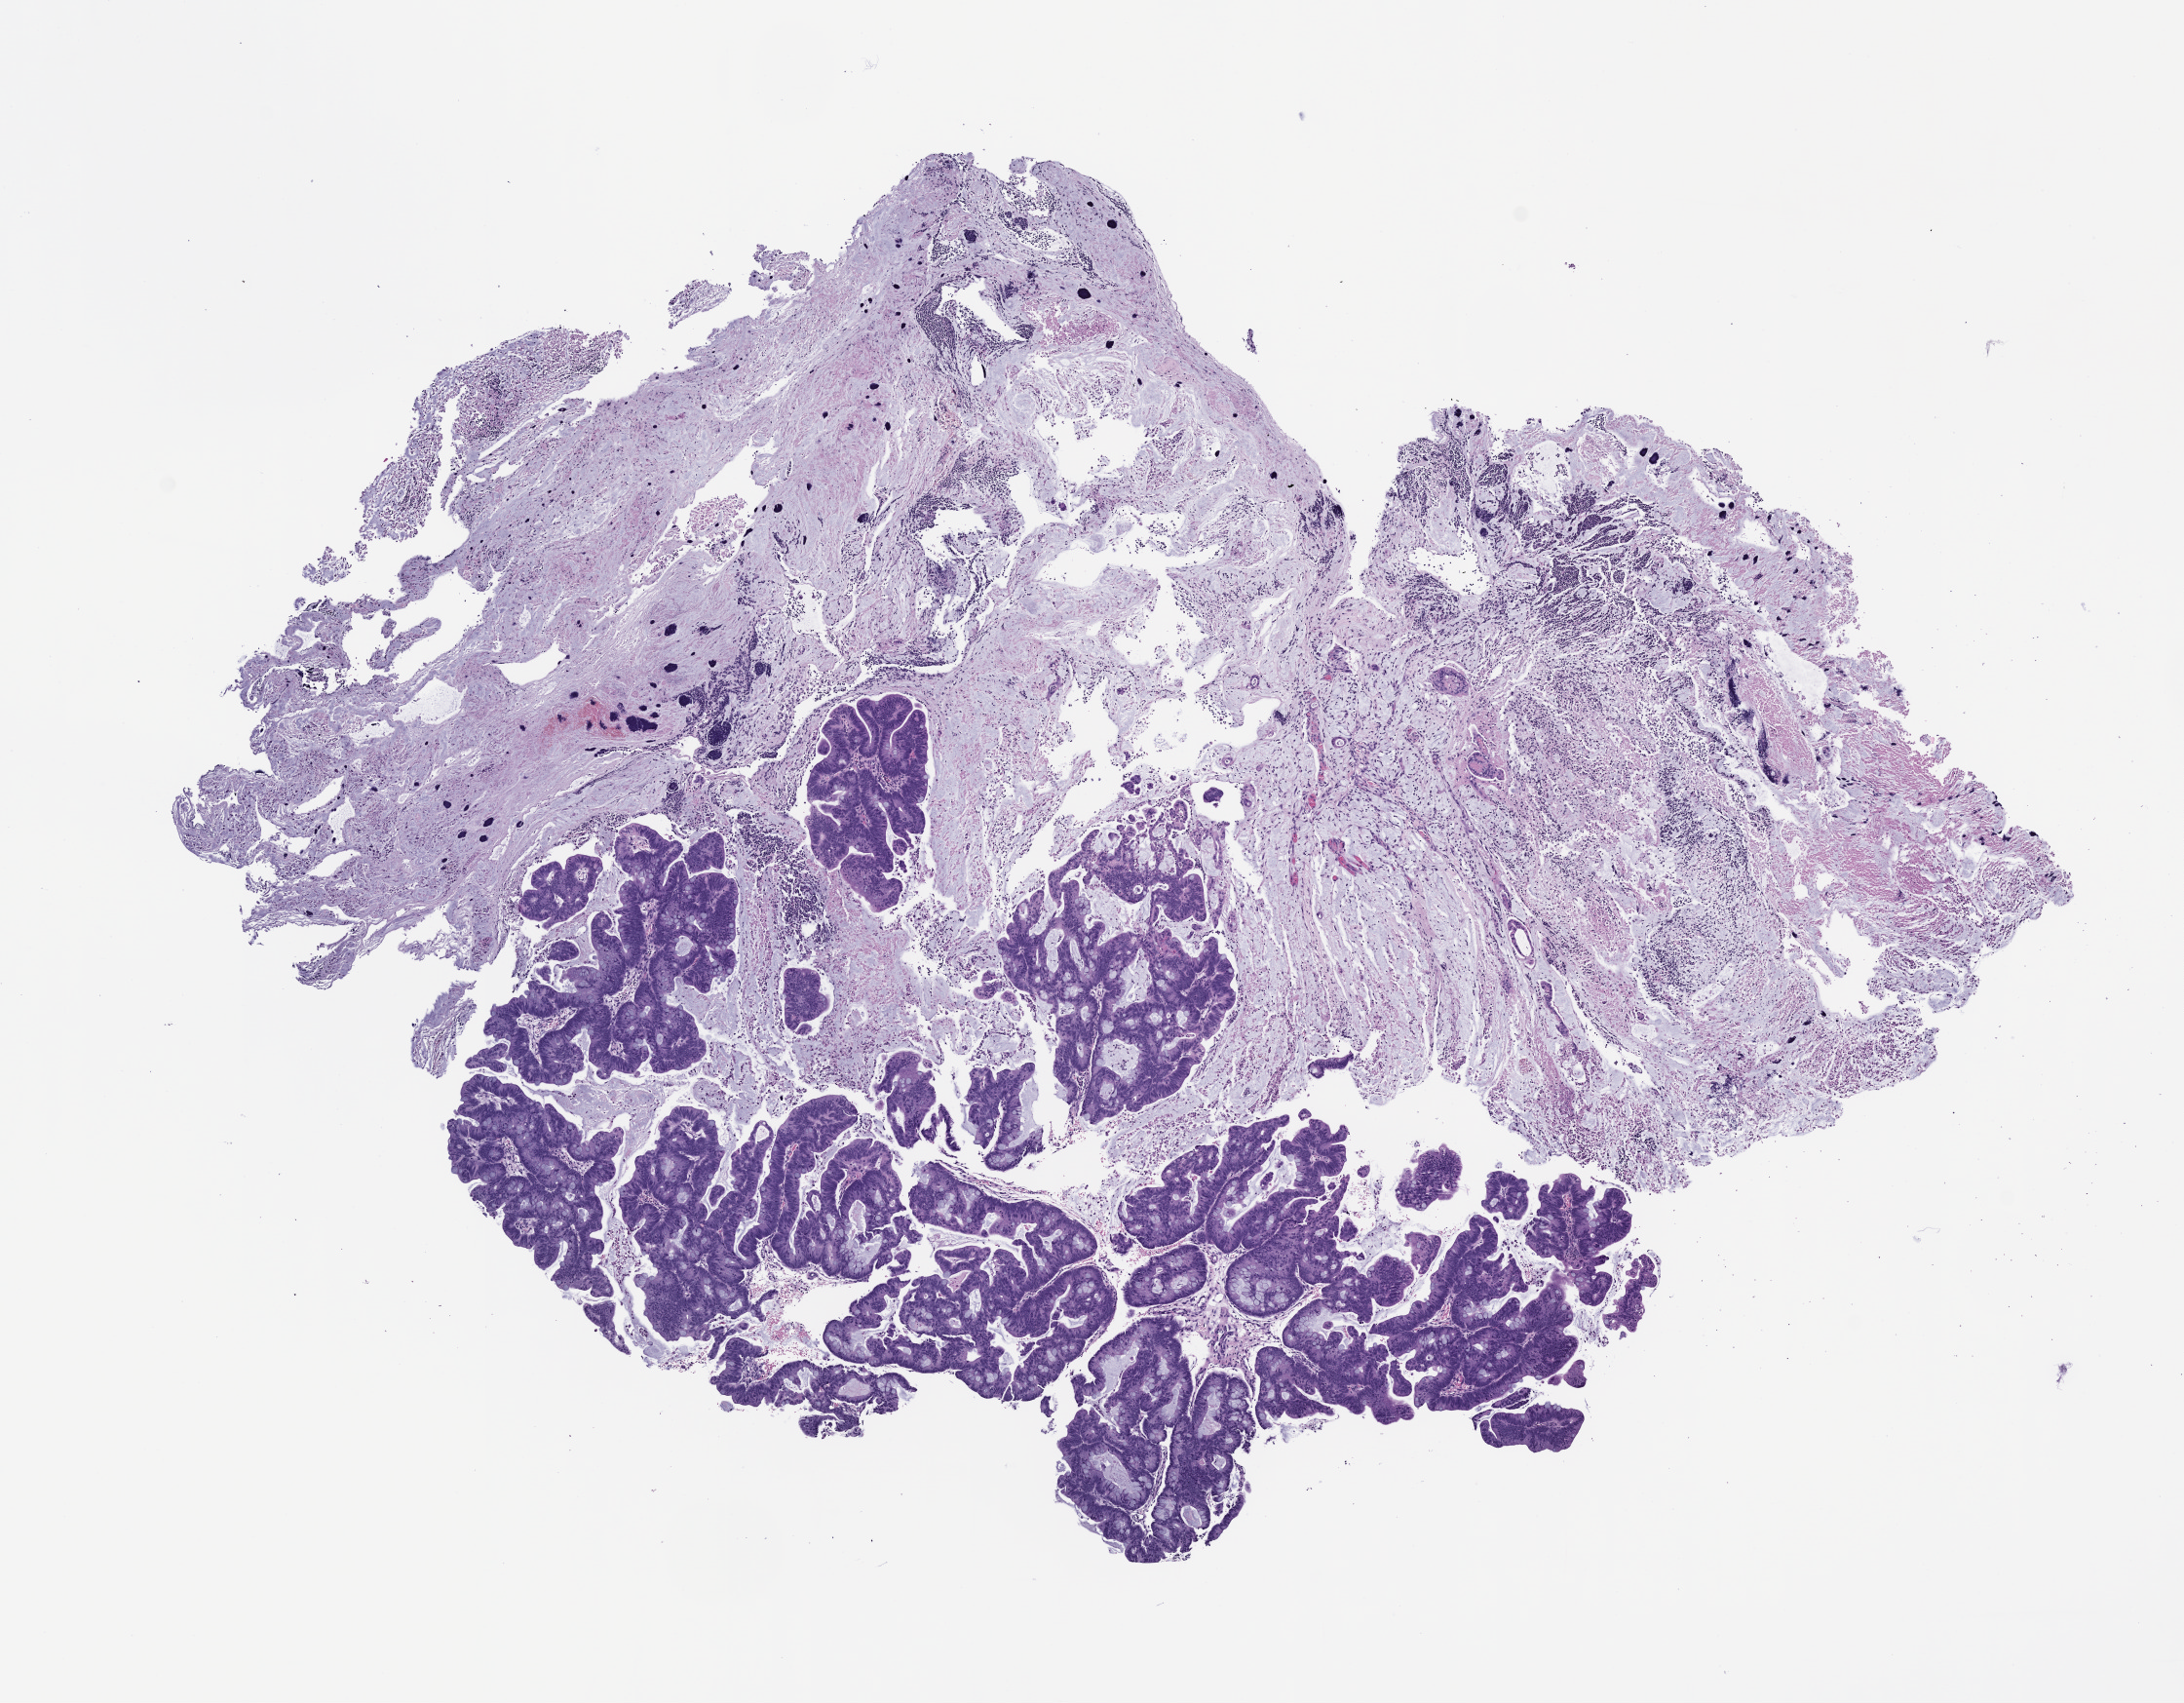
Whole-slide image, hematoxylin and eosin (H&E): patient-derived xenograft (human tumor grown in a mouse), passage 1 — a low-resolution overview of the entire scanned area, about 9.0 x 7.0 mm. FFPE section. Originating tumor site category: colon.
- originating patient diagnosis: Colon Adenocarcinoma